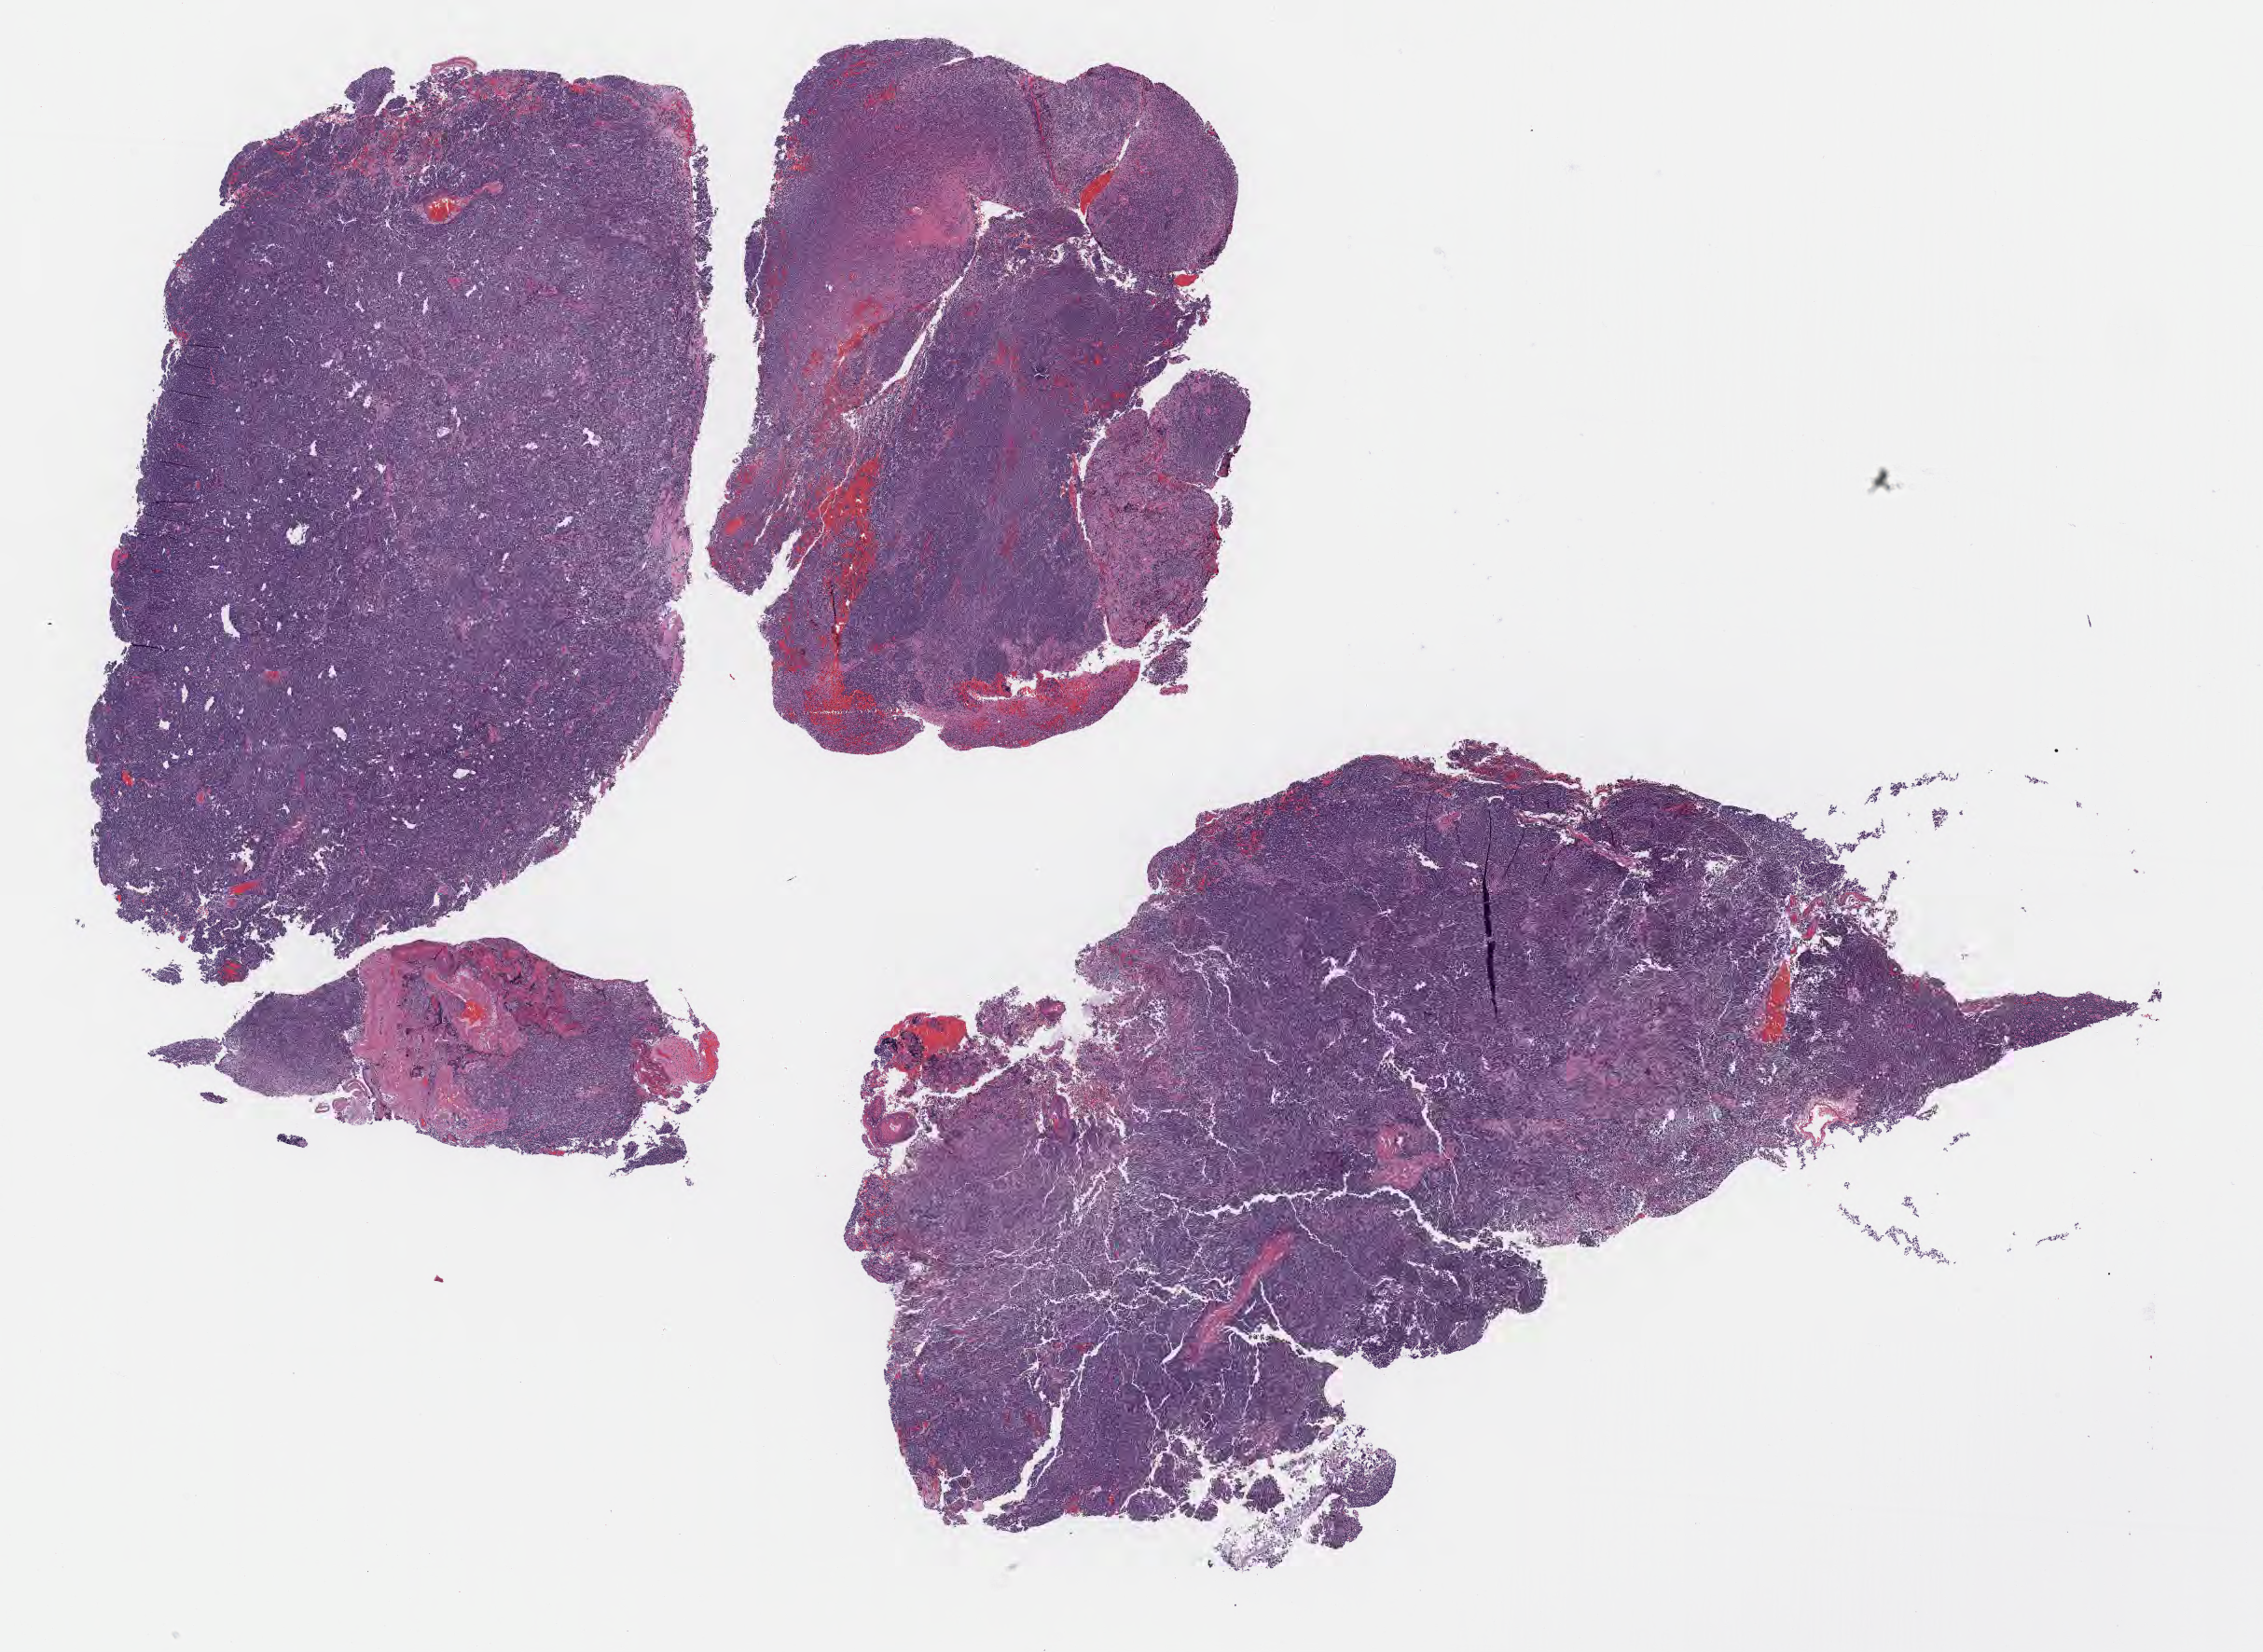
Whole-slide image, hematoxylin and eosin (H&E) stain of tumor tissue from the brain — a low-resolution overview of the entire scanned area, about 19.6 x 14.3 mm. Formalin-fixed, paraffin-embedded (FFPE) tissue. Male patient, age 113 months (9 years 5 months).
Recorded diagnosis: Neoplasm, uncertain whether benign or malignant.